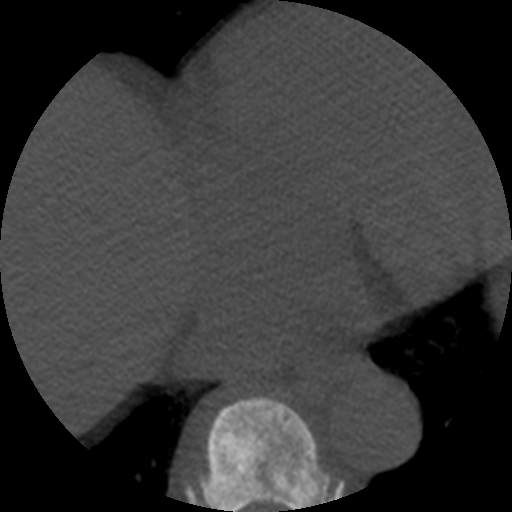
CT including the spine, one axial slice. Slice 307 of 508 in the series (ordered by position). 120 kVp. Bone window (W 1800 / L 400 HU). 1.25 mm slice thickness. 512 × 512 image matrix, field of view 160 × 160 mm. Patient age 57 years. From the clinical record (not read from this slice): primary cancer: prostate.
Outlined on this slice (semi-automatically segmented with operator editing):
- T8 vertebra: box from (x=199, y=396) to (x=331, y=512) px